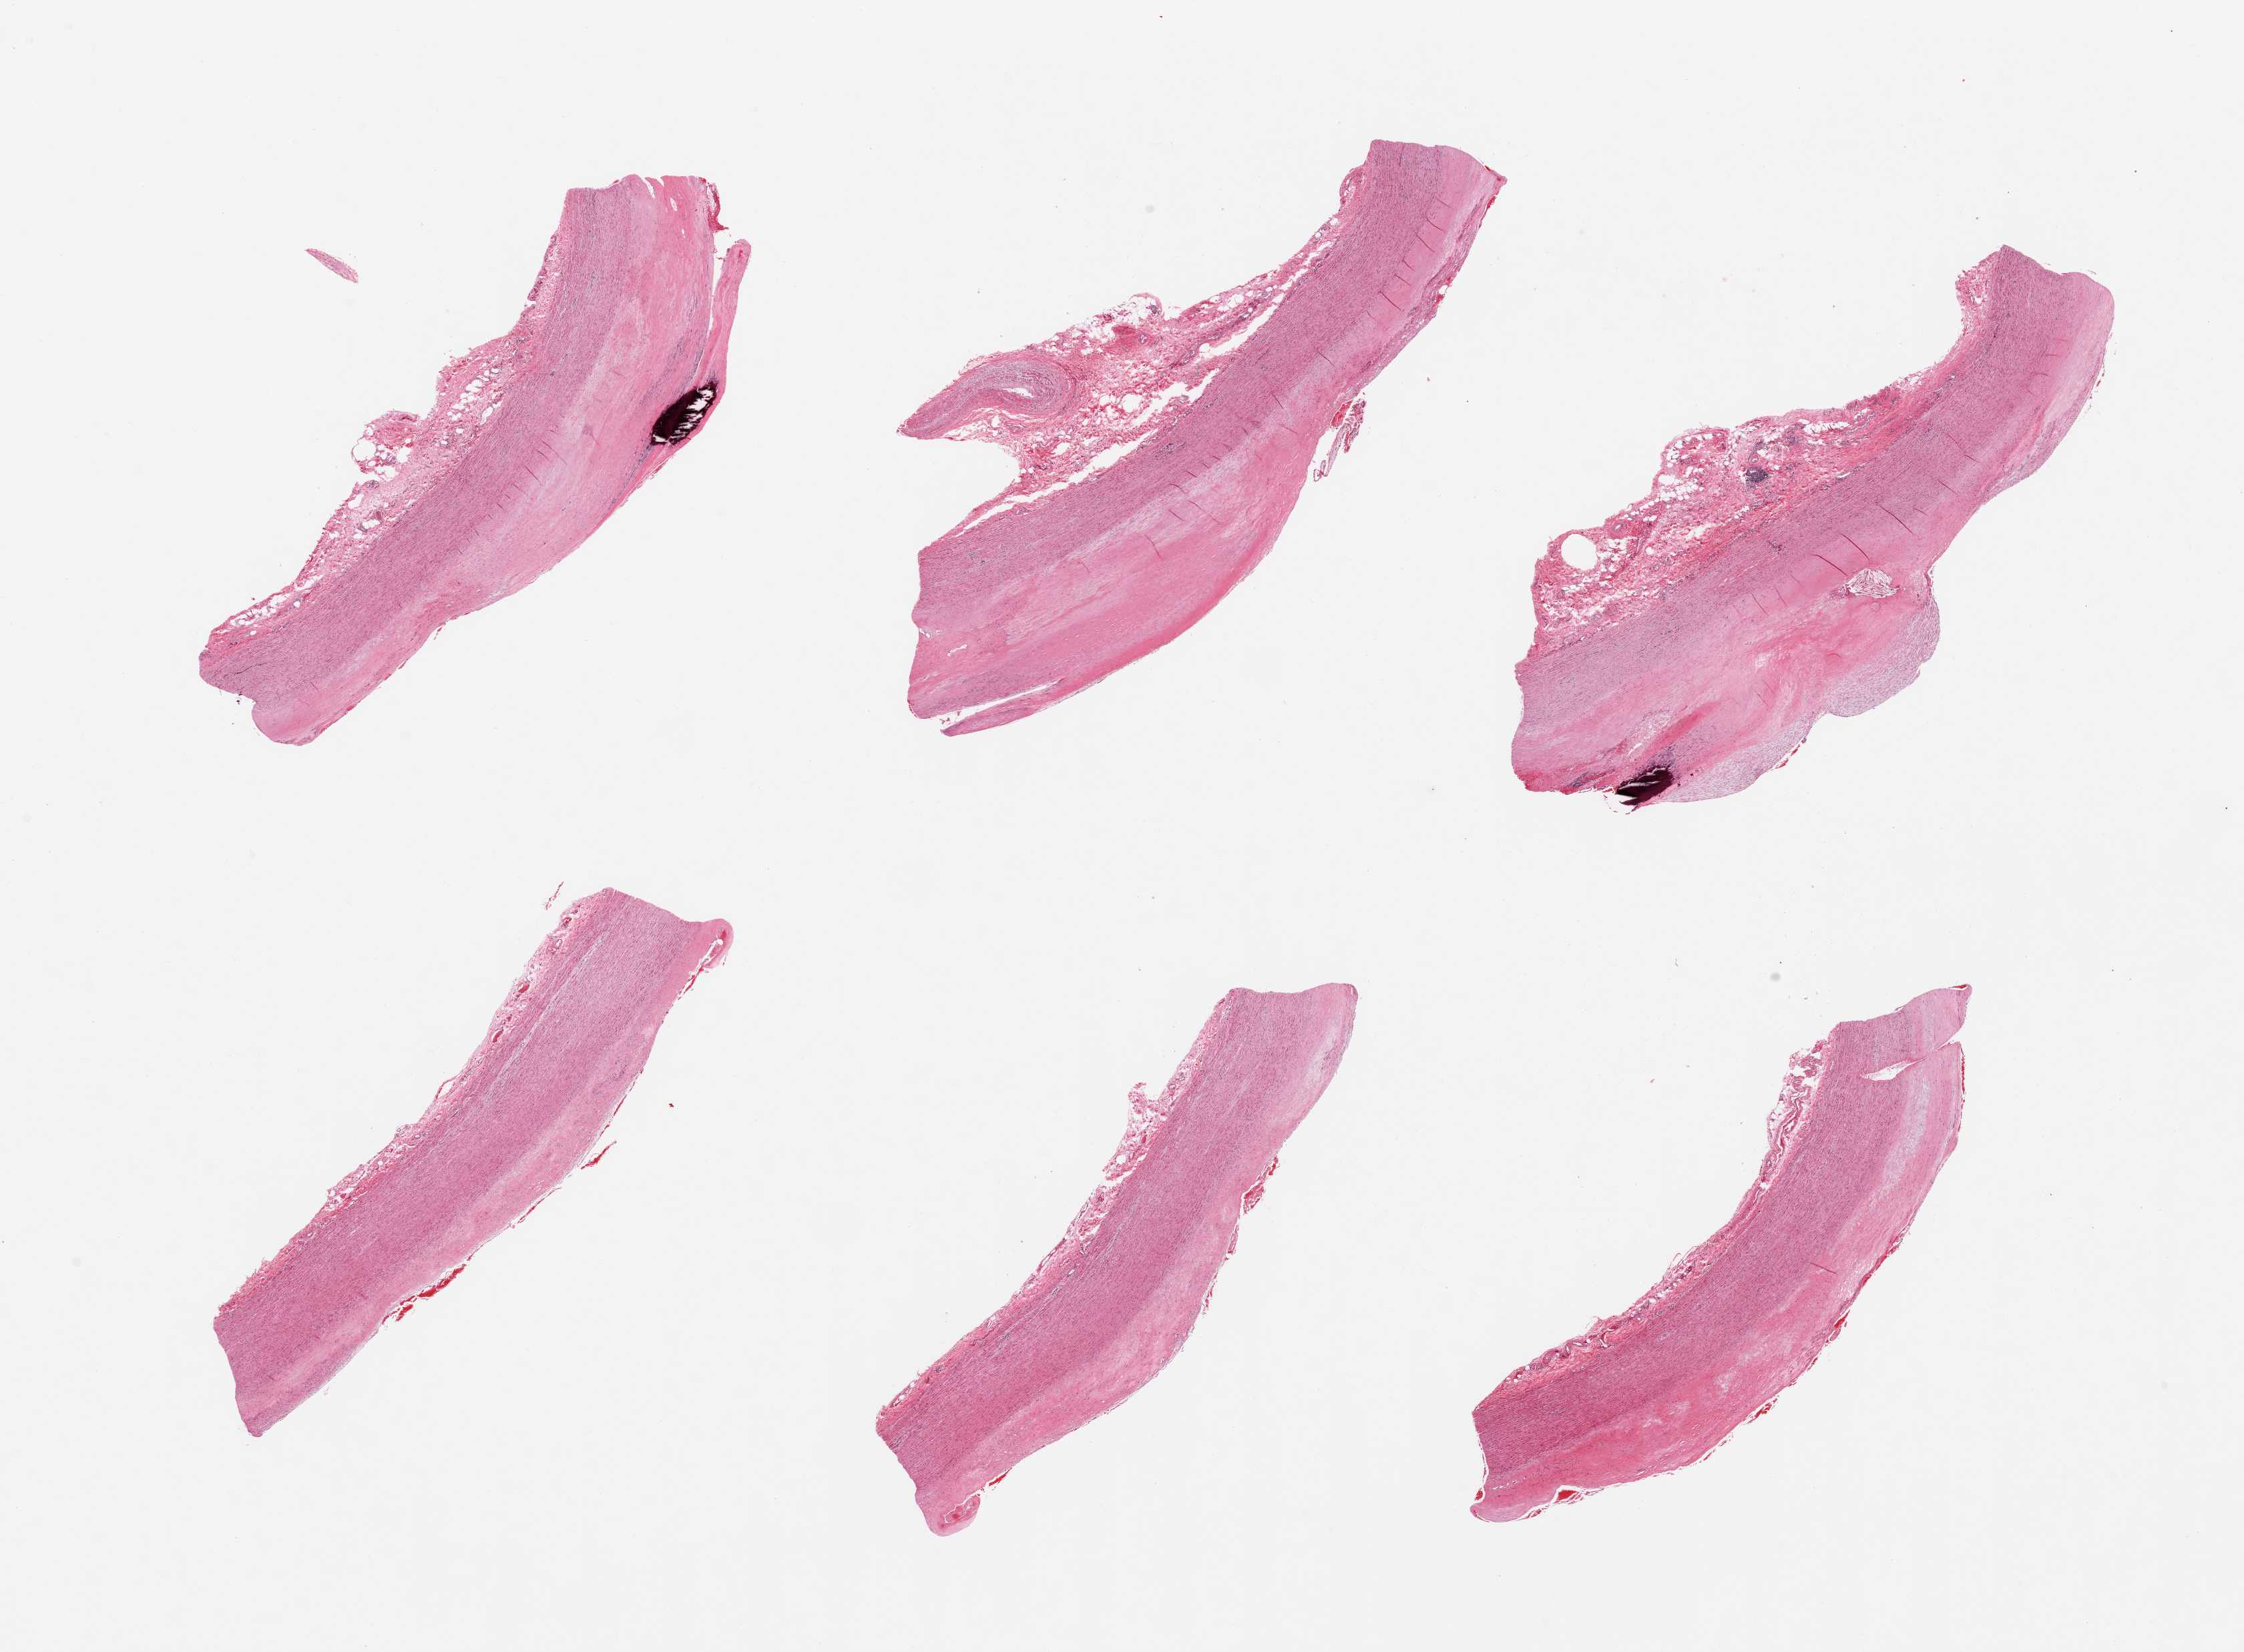
Hematoxylin and eosin (H&E) whole-slide image, a low-resolution overview of the entire scanned area, about 26.6 x 19.6 mm; PAXgene-fixed paraffin-embedded (PFPE) section; section of aorta (target tissue); tissue donor sample. Female donor.
Review note (as recorded): 6 pieces; calcified atheromatous plaques.